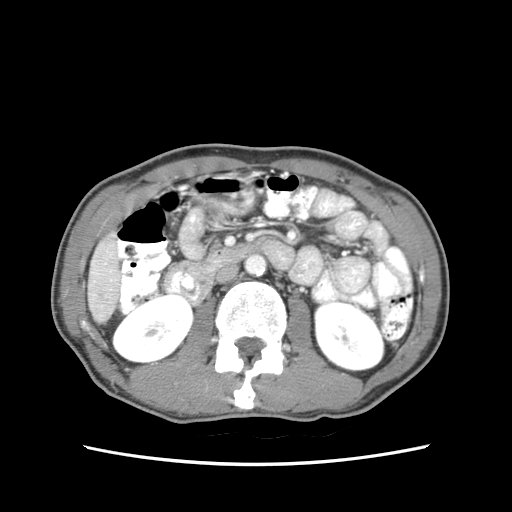
Contrast-enhanced abdominal CT (liver protocol), one axial slice. Position 14 of 79 along the scan axis. Soft-tissue window (W 400 / L 40 HU). 2.5 mm slice thickness. 512 × 512 image matrix, field of view 320 × 320 mm. From the clinical record (not read from this slice): diagnosis: hepatocellular carcinoma (patient treated with transarterial chemoembolisation; whether this scan precedes or follows treatment is not stated here); TNM stage (as recorded): Stage-IIIB; Child-Pugh class: A; tumour nodularity: multinodular.
Outlined on this slice (semi-automatic segmentation, software-assisted and operator-edited):
- liver parenchyma outside the tumour (the mass and vessels are separate outlines, so this box may not span the whole liver): bounding box (x1, y1, x2, y2) in pixels: (88, 233, 120, 320)
- liver vessels: (110, 269, 113, 272)